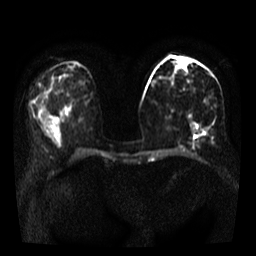
Breast MRI, one axial slice. Position 17 of 35 along the scan axis. Diffusion-weighted series; image 2 of 4 stored at this slice position (different b-values; order by instance number). 3 T. 256 × 256 image matrix, field of view 320 × 320 mm. Female patient.
Annotated regions visible in this slice (manually delineated by an expert):
- tumour on diffusion-weighted imaging: bounding box (x1, y1, x2, y2) in pixels: (193, 130, 207, 138)